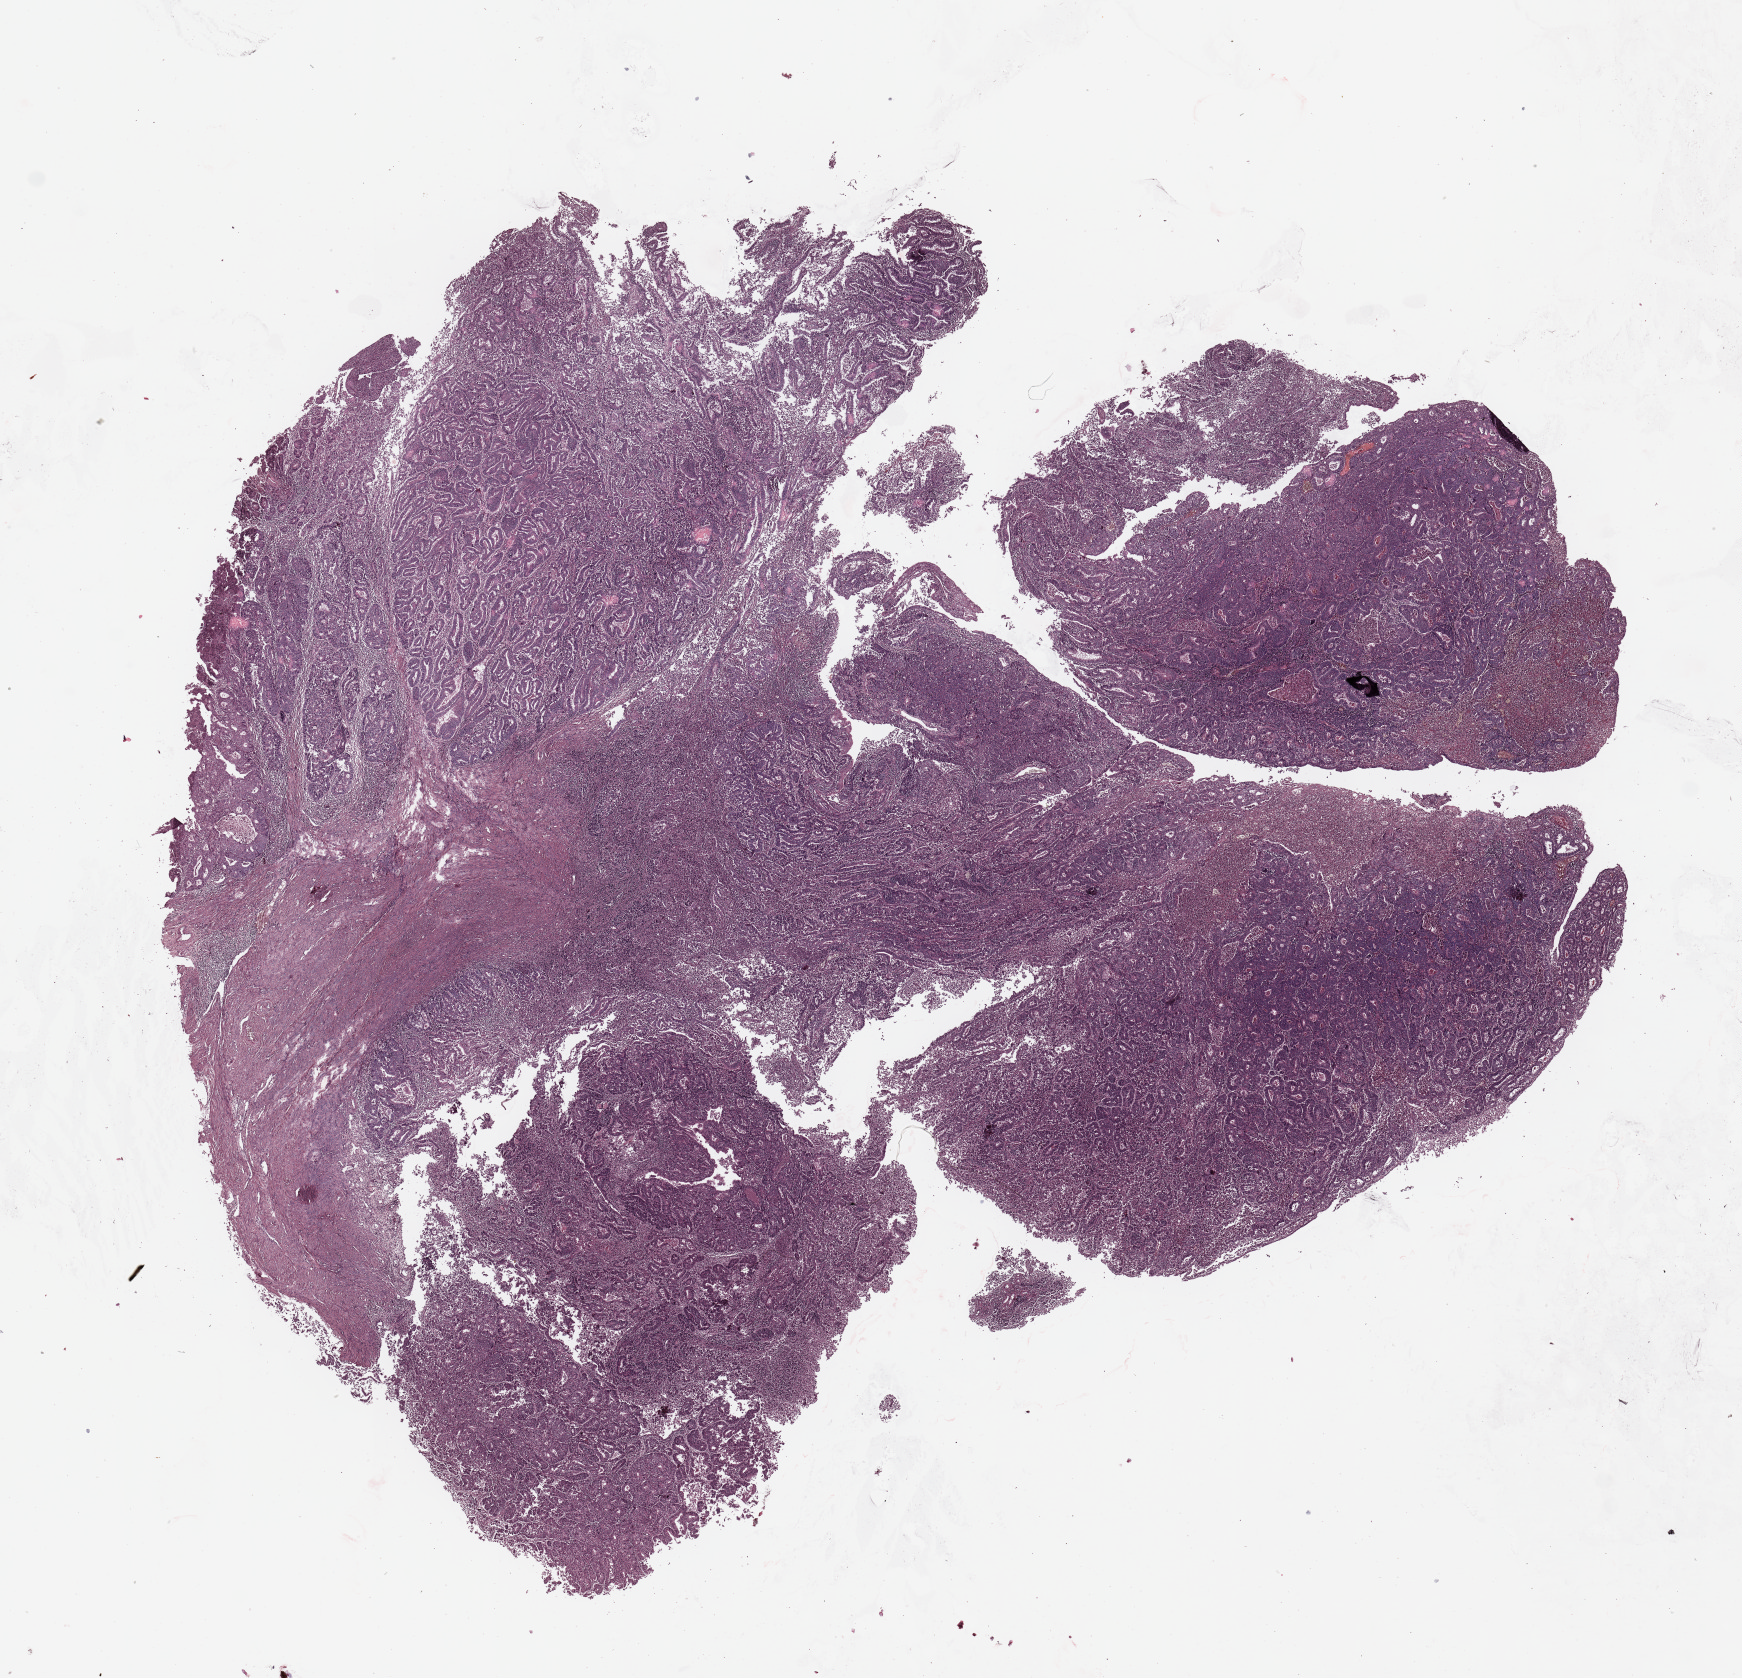
Whole-slide histology image, Hematoxylin and eosin (H&E) stained — shown as a low-resolution overview of the whole scanned area (about 13.8 x 13.3 mm, slide scanned at 20x). Uterus, tumour tissue. 69-year-old female patient. Histologic grade: G2 (moderately differentiated).
- diagnosis: Endometrioid adenocarcinoma, NOS
- AJCC pathologic stage: I